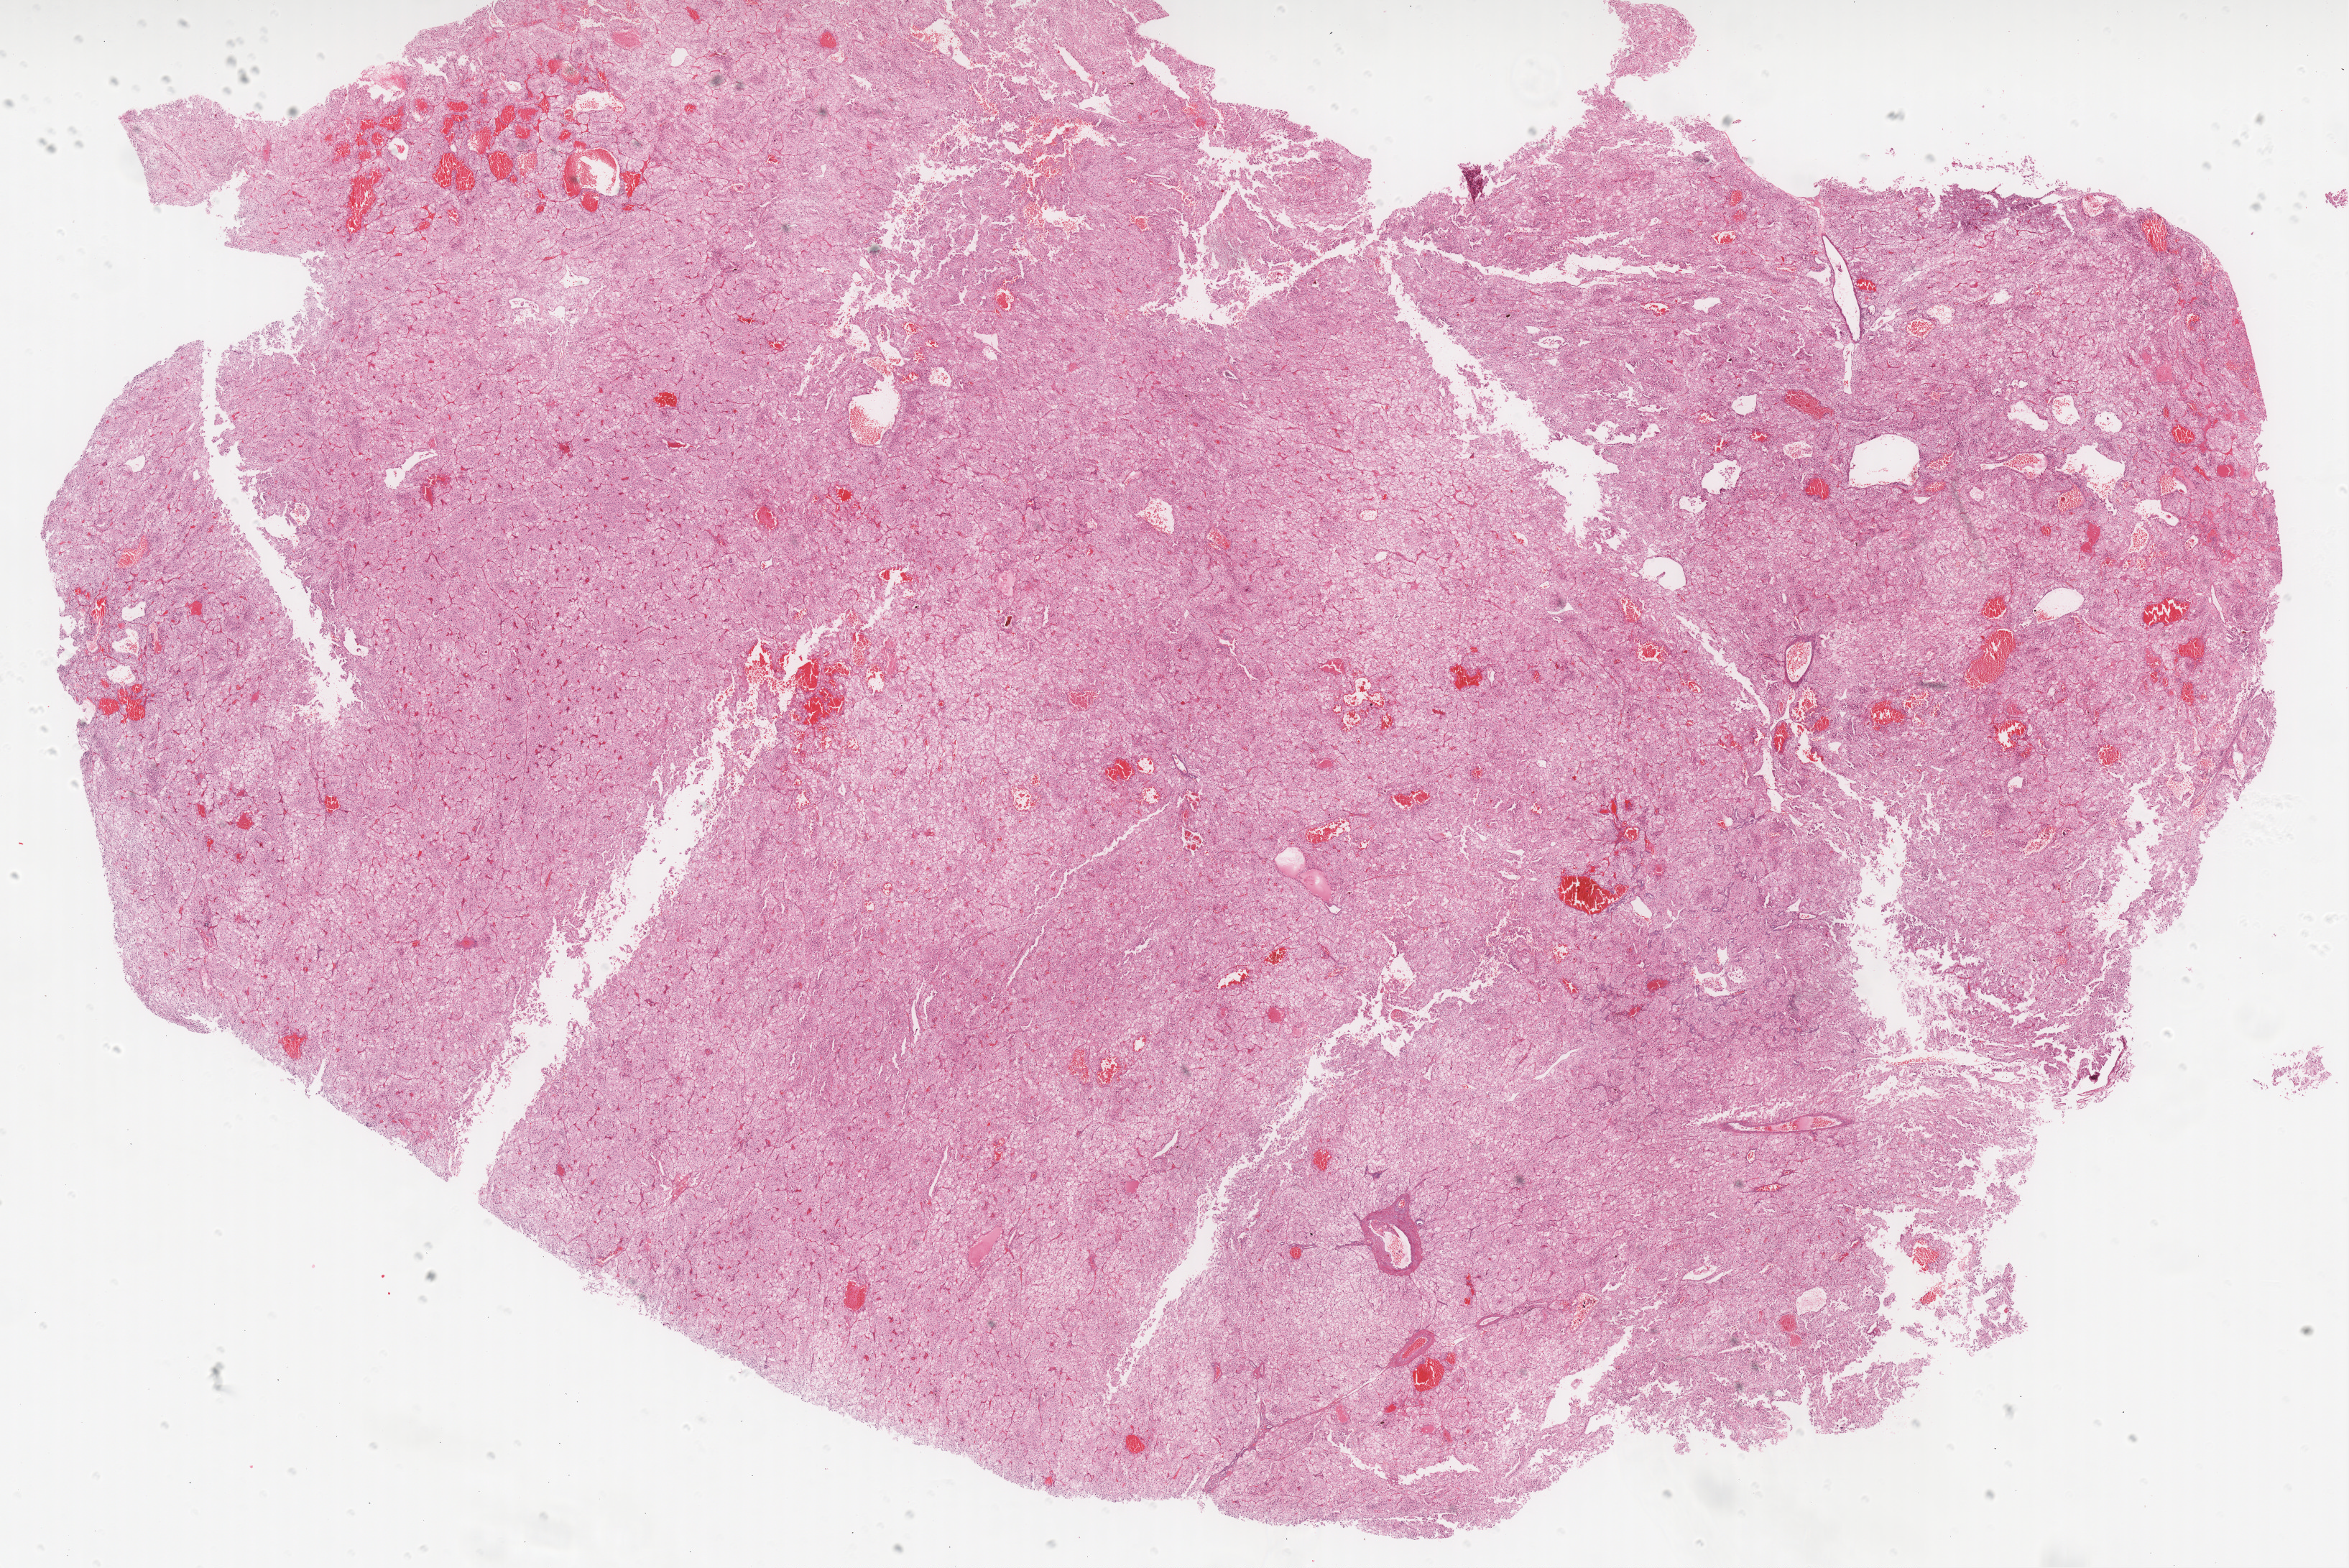
H&E whole-slide image, a low-resolution overview of the entire scanned area, about 26.1 x 17.4 mm, formalin-fixed paraffin-embedded (FFPE) diagnostic section, primary tumour sample from the kidney. Female patient; age at initial diagnosis 46 years.
- pathologic diagnosis: Renal cell carcinoma, chromophobe type
- AJCC pathologic stage: I (5th edition)
- lymph nodes positive (case pathology): 0 of 3 examined